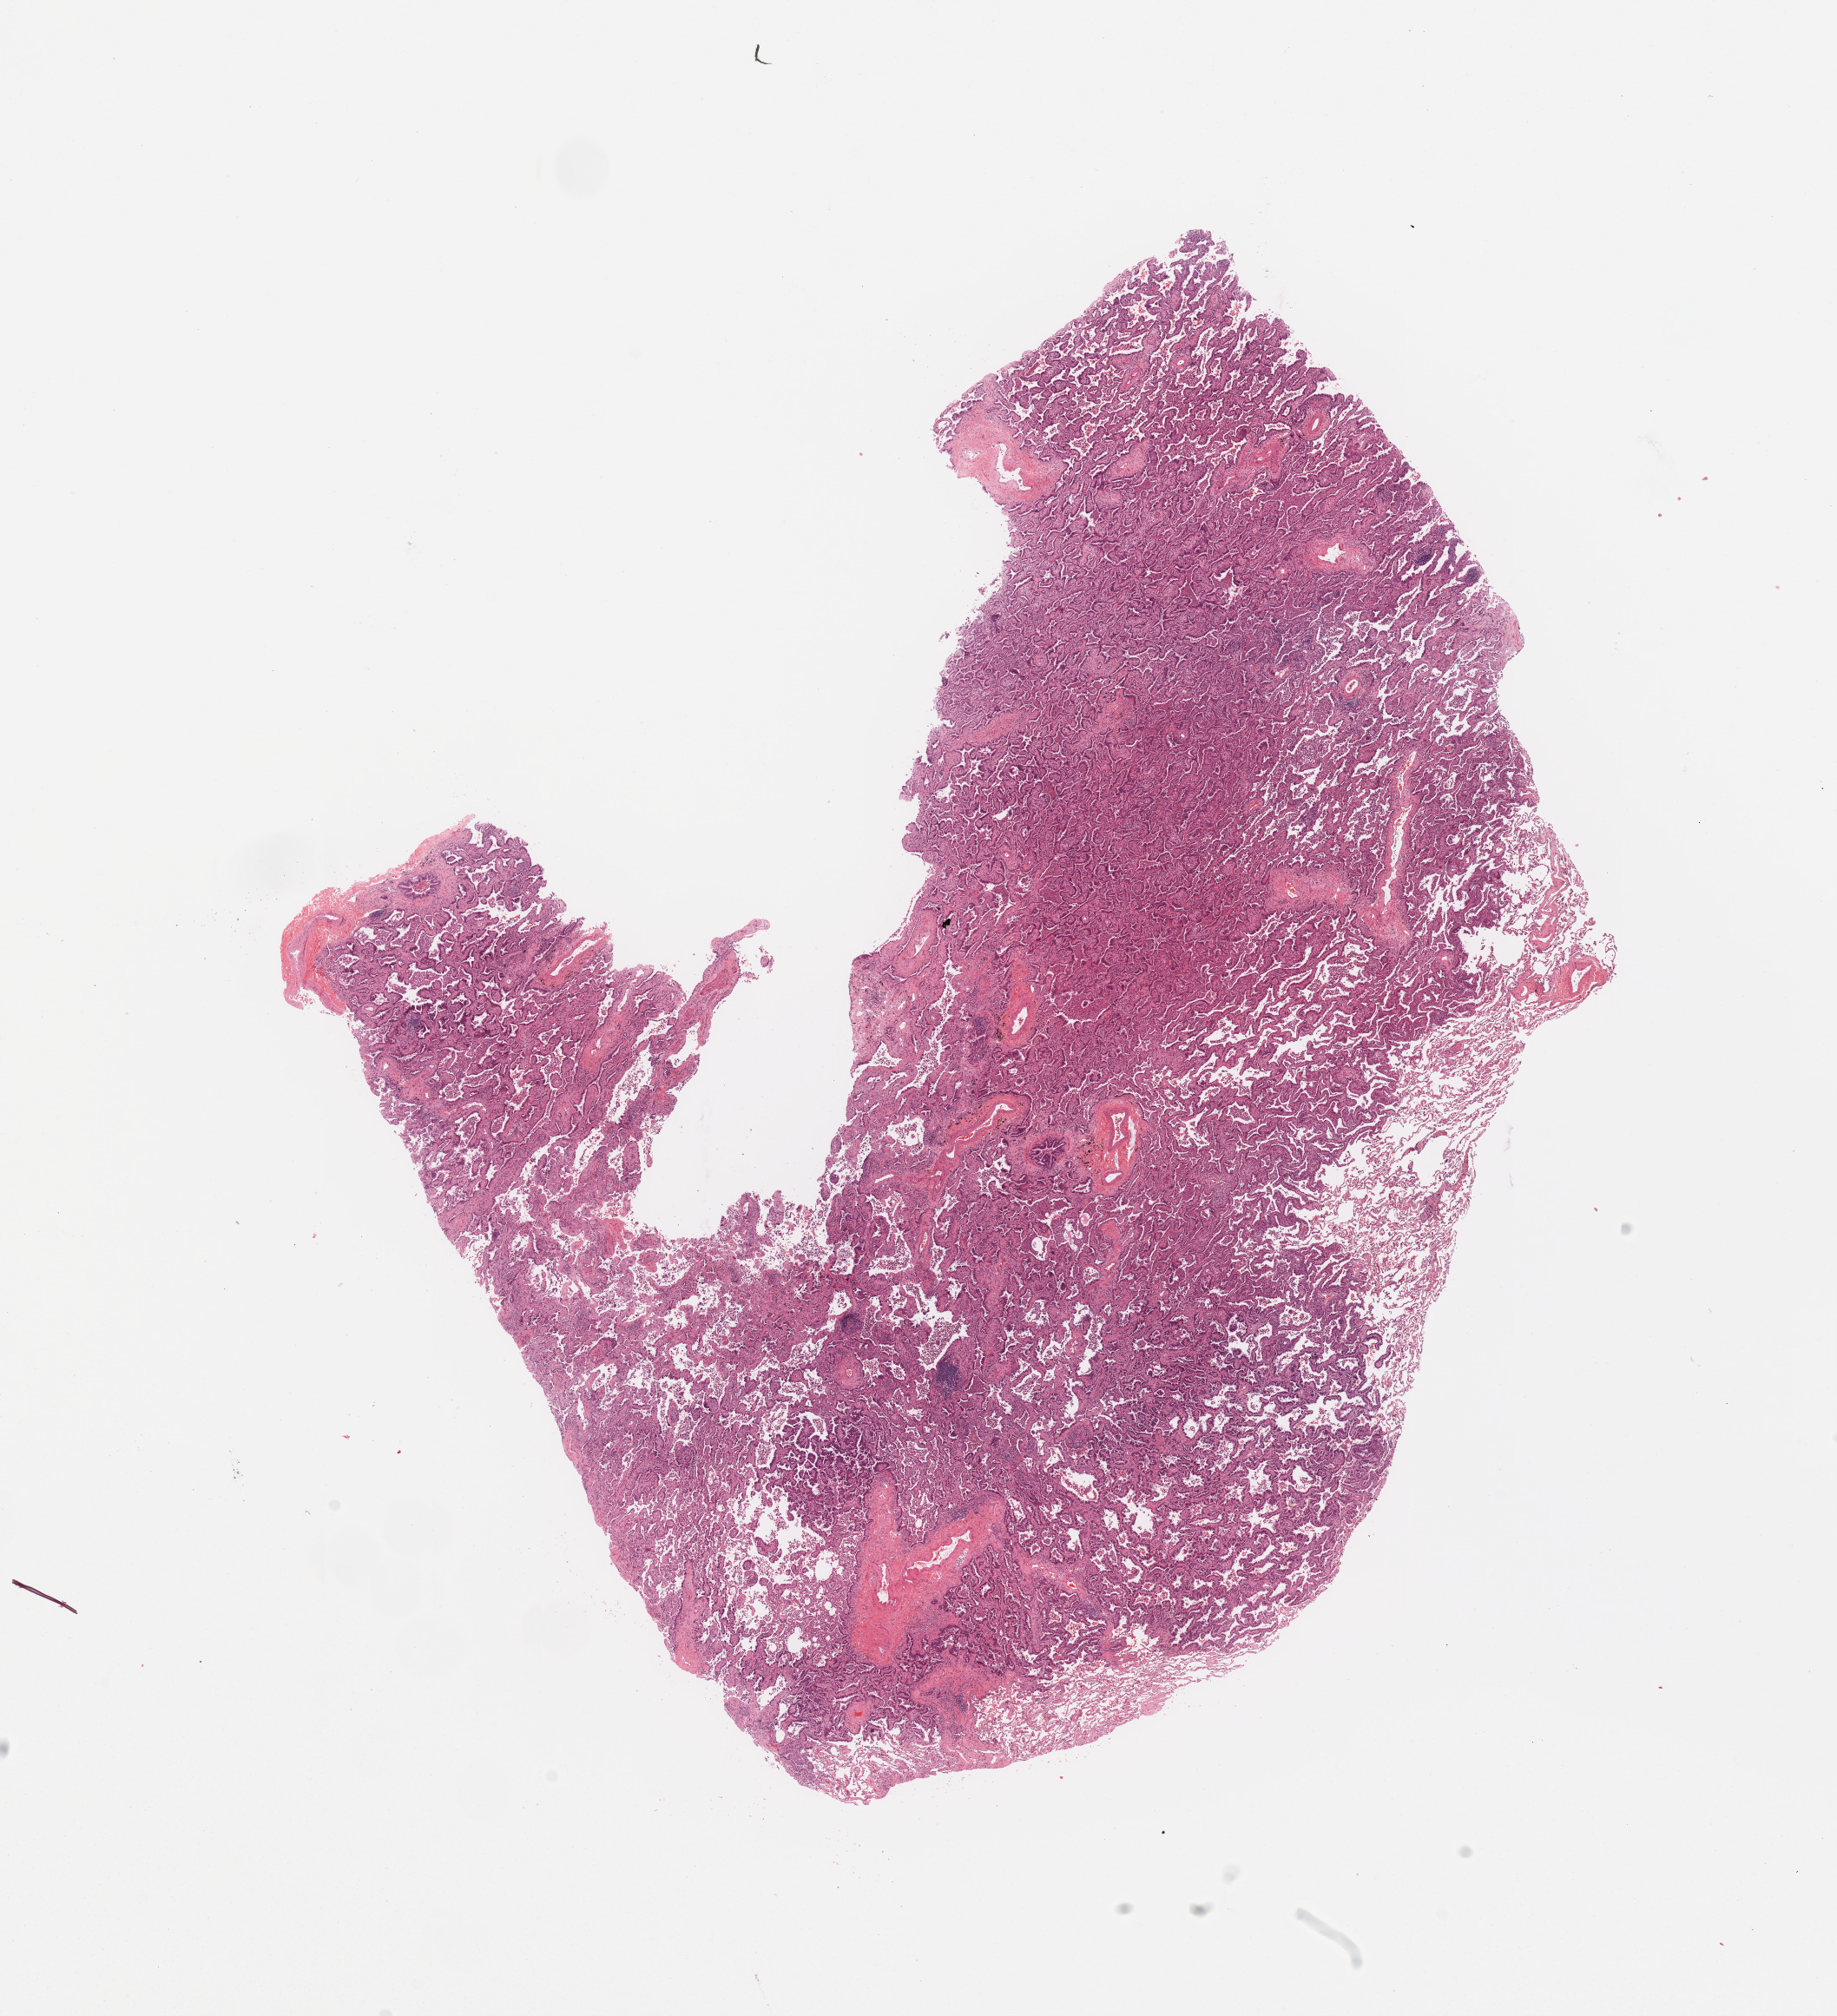
Whole-slide histology image, H&E, low-resolution overview of the scanned area, about 16.7 x 18.4 mm (slide scanned at 20x); tumour tissue sample, sampled site: lung. Male, 56 y/o. Histologic grade: G2 (moderately differentiated). Pathologist review of this section (percent, as recorded): tumour nuclei 70%, necrosis 2%.
Primary tumour site (as recorded): right lower lobe. AJCC pathologic stage: IB. Histologic diagnosis: Adenocarcinoma, NOS.